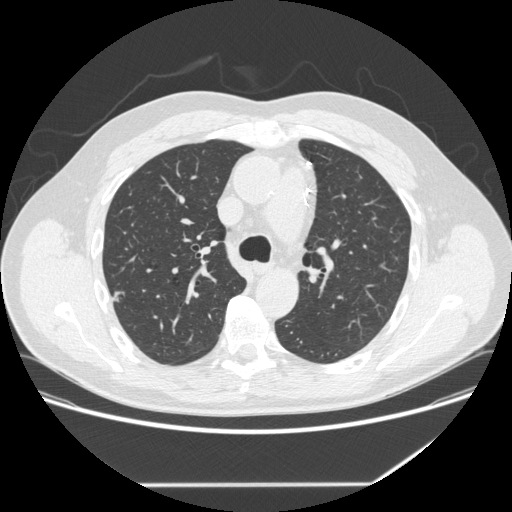
Low-dose screening chest CT, axial slice, baseline annual screen, lung window (W 1500 / L -600 HU), 1.25 mm slice thickness, standard (soft-tissue) reconstruction kernel (STANDARD), slice 90 of 262 in the series. Male, age 62 years at enrolment.
• Expert-annotated lung lesion, bounding box <101,280,132,313> (left, top, right, bottom; pixels).
• Screening reader's record for this exam: no non-calcified nodule ≥4 mm recorded.
• Official screen result: negative screen, minor abnormalities not suspicious for lung cancer.